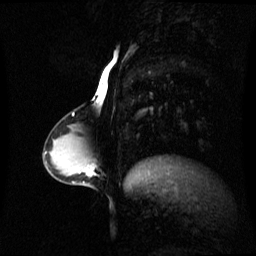
Breast MRI (dynamic contrast-enhanced), one sagittal slice. Slice 26 of 60 in the series (ordered by position). Dynamic contrast-enhanced series, image 2 of 3 at this slice position (ordered by acquisition). 1.5 T. TE 4.2 ms, TR 8.4 ms. 256 × 256 image matrix. Patient: female, 34 years. Case-level facts recorded for this patient, not image findings: setting: breast cancer imaged before/during neoadjuvant chemotherapy; receptor status: triple-negative.
Structures marked on this image (semi-automatic segmentation, software-assisted and operator-edited):
- analysis volume of interest (the breast-tissue region the enhancement analysis was run in; not a lesion): bounding box [x1, y1, x2, y2] px = [57, 156, 95, 187]
- tumour enhancement mask (voxels above the 70 % enhancement threshold inside the analysis volume of interest): [86, 170, 92, 175]